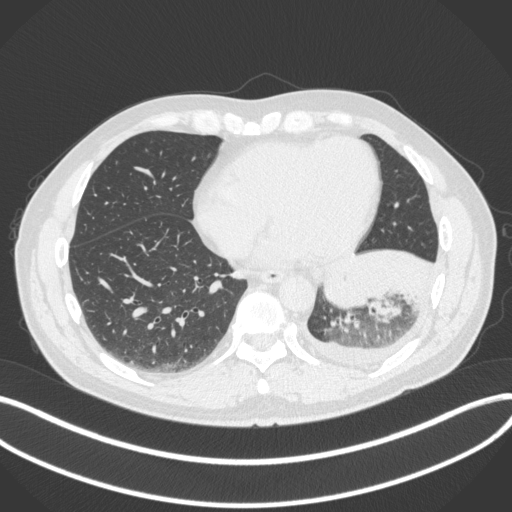
Chest CT, one axial slice. Position 117 of 350 along the scan axis. 120 kVp. Lung window (W 1500 / L -600 HU). 1 mm slice thickness. 512 × 512 image matrix, field of view 400 × 400 mm. Male patient, age 58 years. From the clinical record (not read from this slice): clinical TNM (as recorded): T3 N1 M1b.
Annotated regions visible in this slice (bounding box drawn by a radiologist):
- lung tumour (recorded histology: small cell carcinoma): bounding box [x1, y1, x2, y2] px = [323, 253, 373, 315]